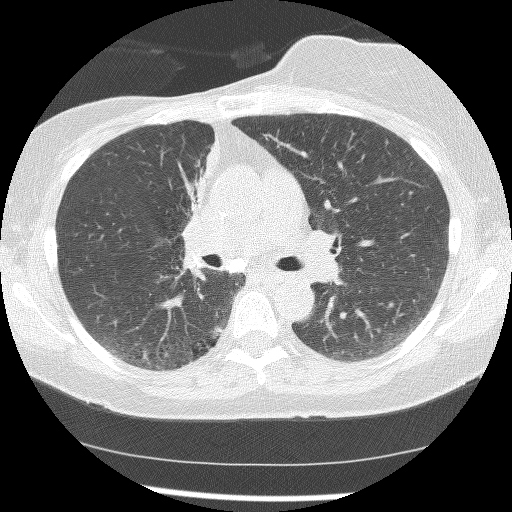
Chest CT (low-dose screening protocol), one axial image. First (baseline) screen. Lung window (W 1500 / L -600 HU). 2.5 mm slice thickness. 120 kVp. 512 × 512 image matrix, field of view 315 × 315 mm. Female, age 56 years at enrolment.
Lesion marked by an expert reader, bounding box (x1, y1, x2, y2) in pixels: (161, 139, 216, 255). The screening reader recorded 2 non-calcified nodules or masses ≥4 mm on this exam (right lower lobe, right middle lobe); which of them this box marks is not recorded. Official screen result: positive, change unspecified: nodule(s) >= 4 mm or enlarging nodule(s), mass(es), or other non-specific abnormalities suspicious for lung cancer. Later outcome: lung cancer diagnosed 1185 days after this screen — adenocarcinoma, NOS, right upper lobe, stage IIIB (AJCC 6th edition), 8 mm at pathology.